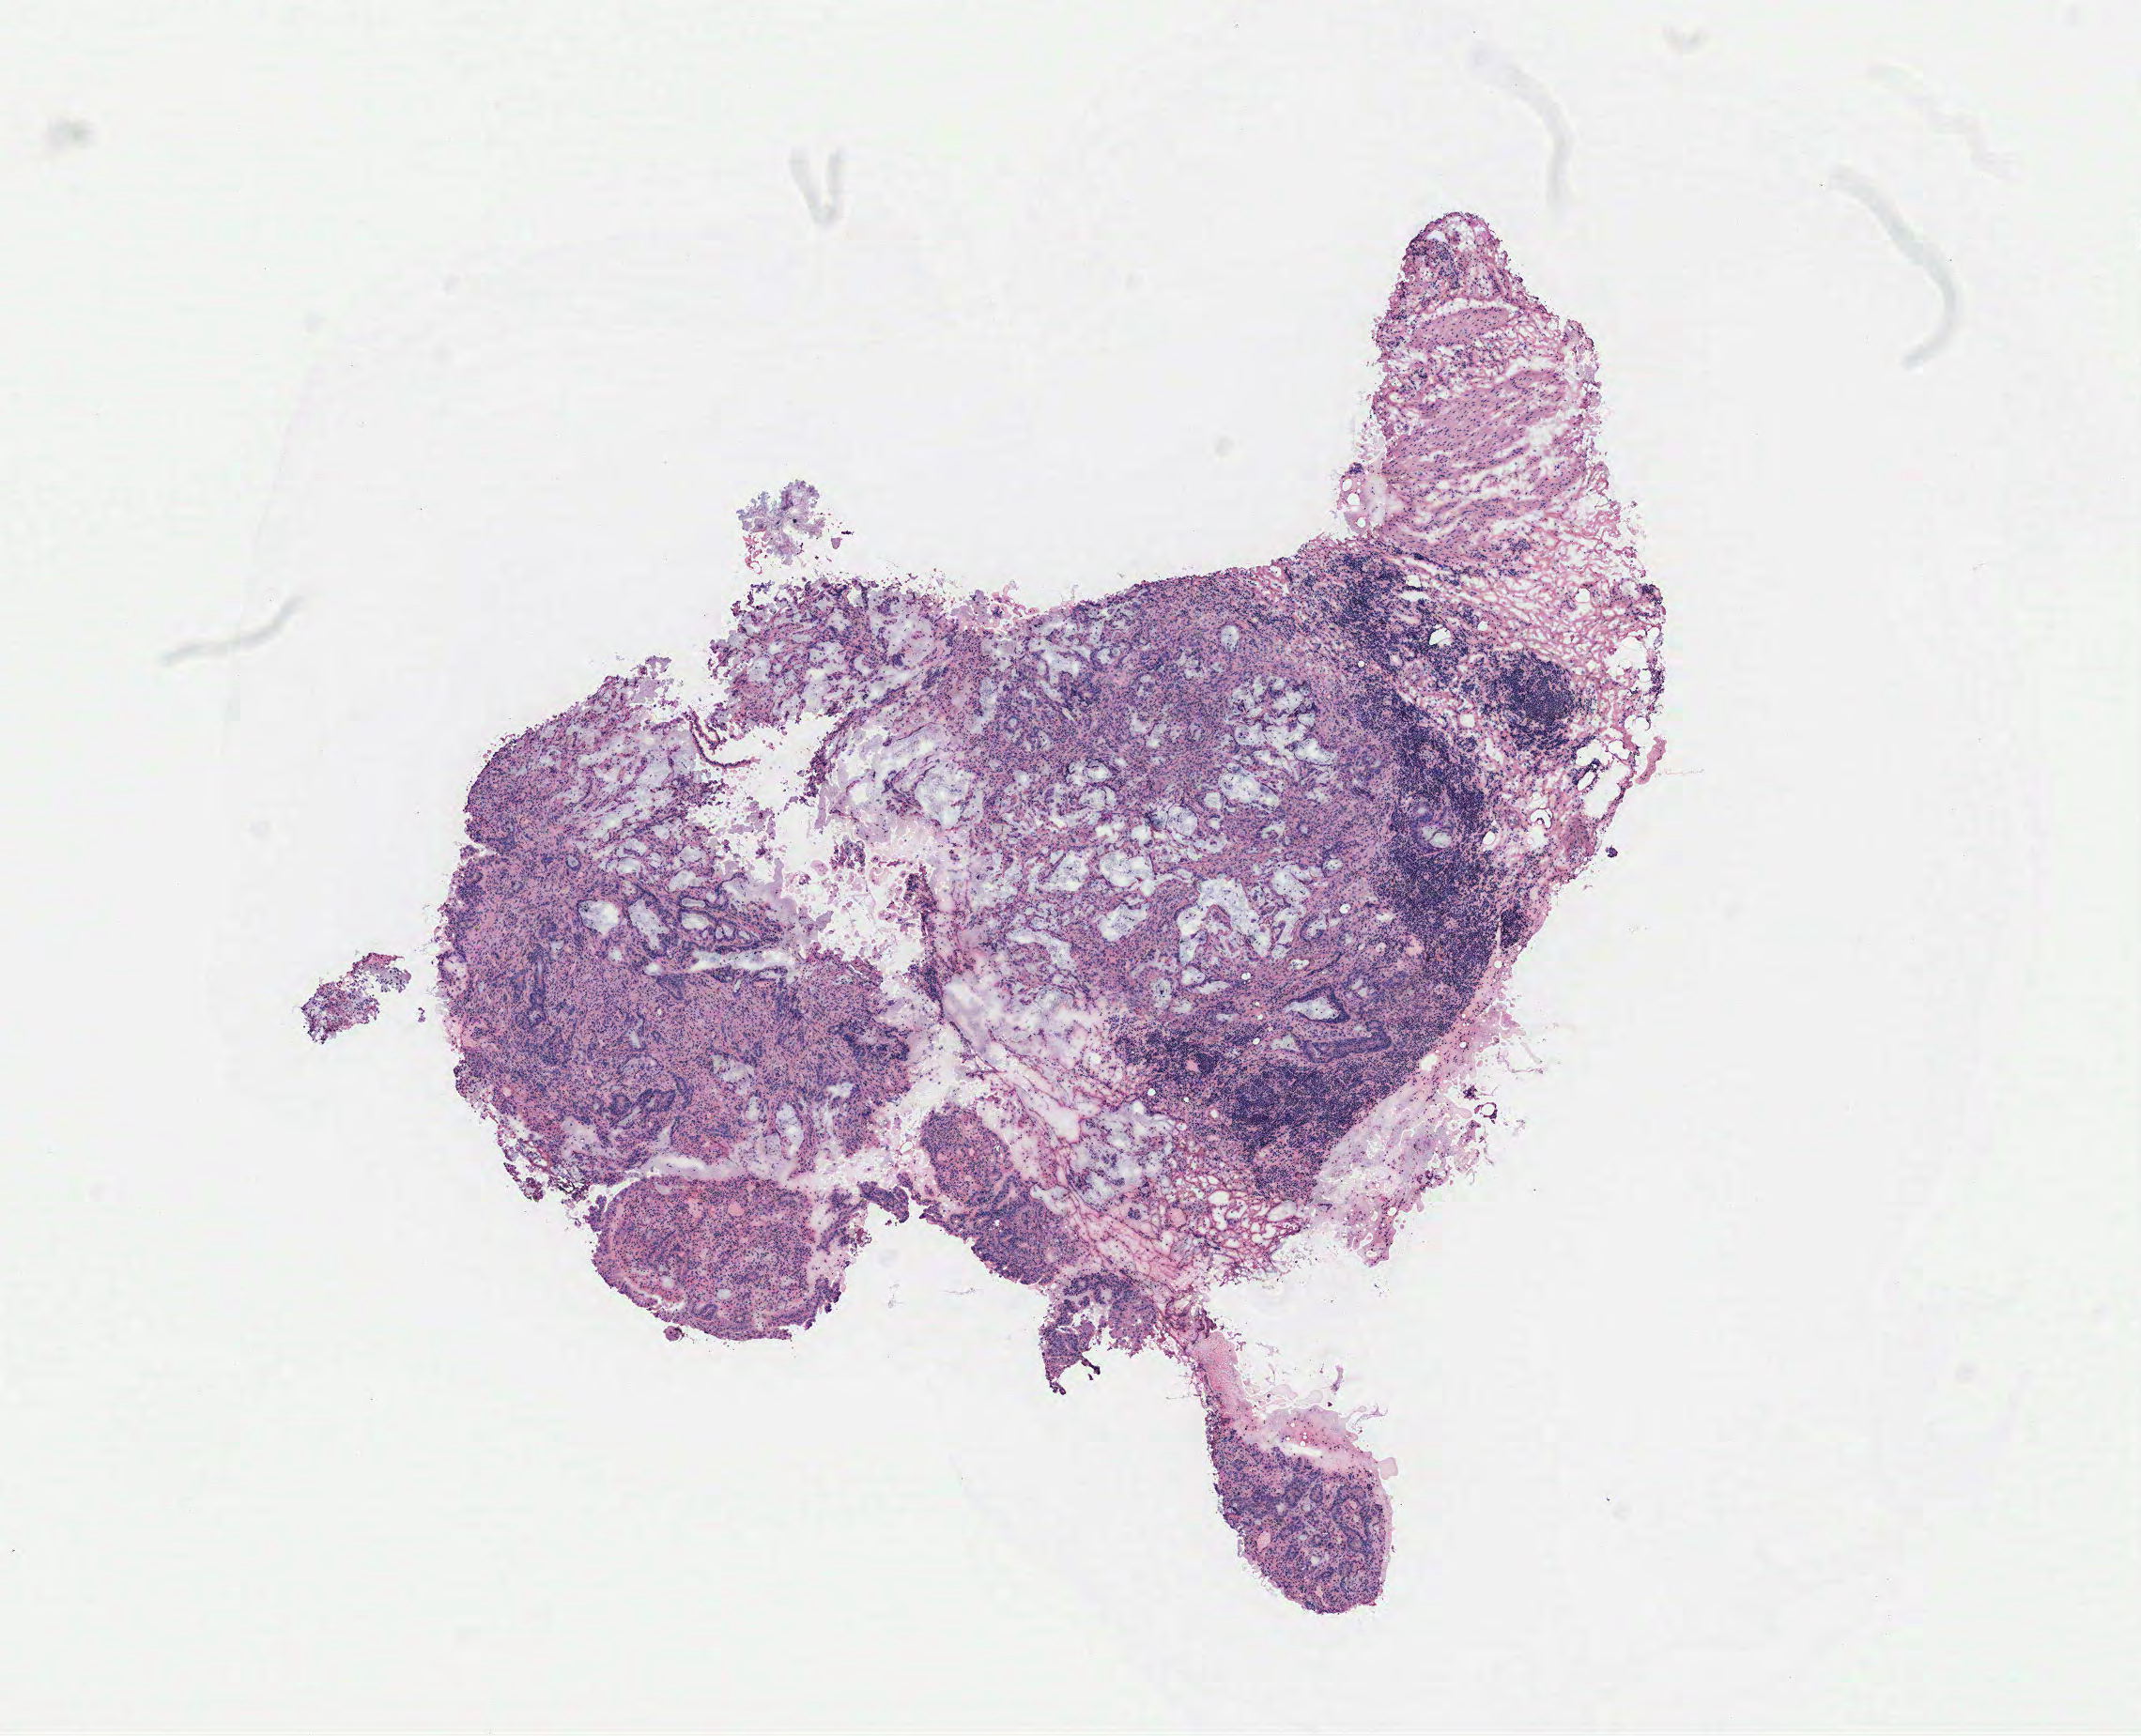
Hematoxylin and eosin (H&E) stained whole-slide image — low-resolution overview of the scanned area, about 9.1 x 7.4 mm (slide scanned at 40x), tumour tissue sample, colon. 61-year-old male patient.
• diagnosis: Adenocarcinoma, NOS
• AJCC pathologic stage: IIIC
• primary tumour site (as recorded): colon